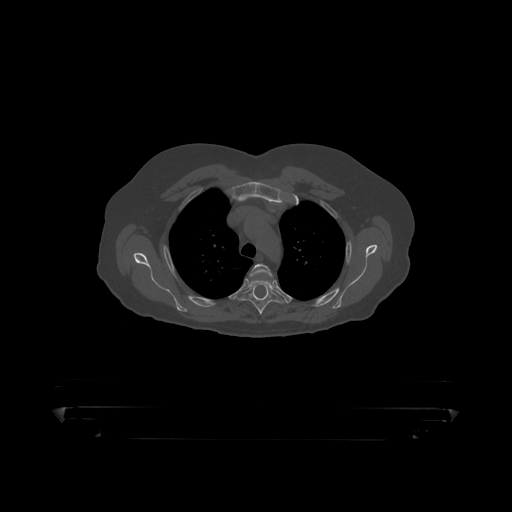
CT including the spine, one axial slice. Slice 343 of 390 in the series (ordered by position). Reconstruction kernel STANDARD. 120 kVp. Bone window (W 1800 / L 400 HU). 1.25 mm slice thickness. 512 × 512 image matrix, field of view 650 × 650 mm. Patient: male, 60 years. From the clinical record (not read from this slice): primary cancer: prostate.
Structures marked on this image (semi-automatic segmentation, software-assisted and operator-edited):
- T3 vertebra: box from (x=250, y=264) to (x=273, y=287) px
- T4 vertebra: (x=238, y=280)–(x=284, y=316)